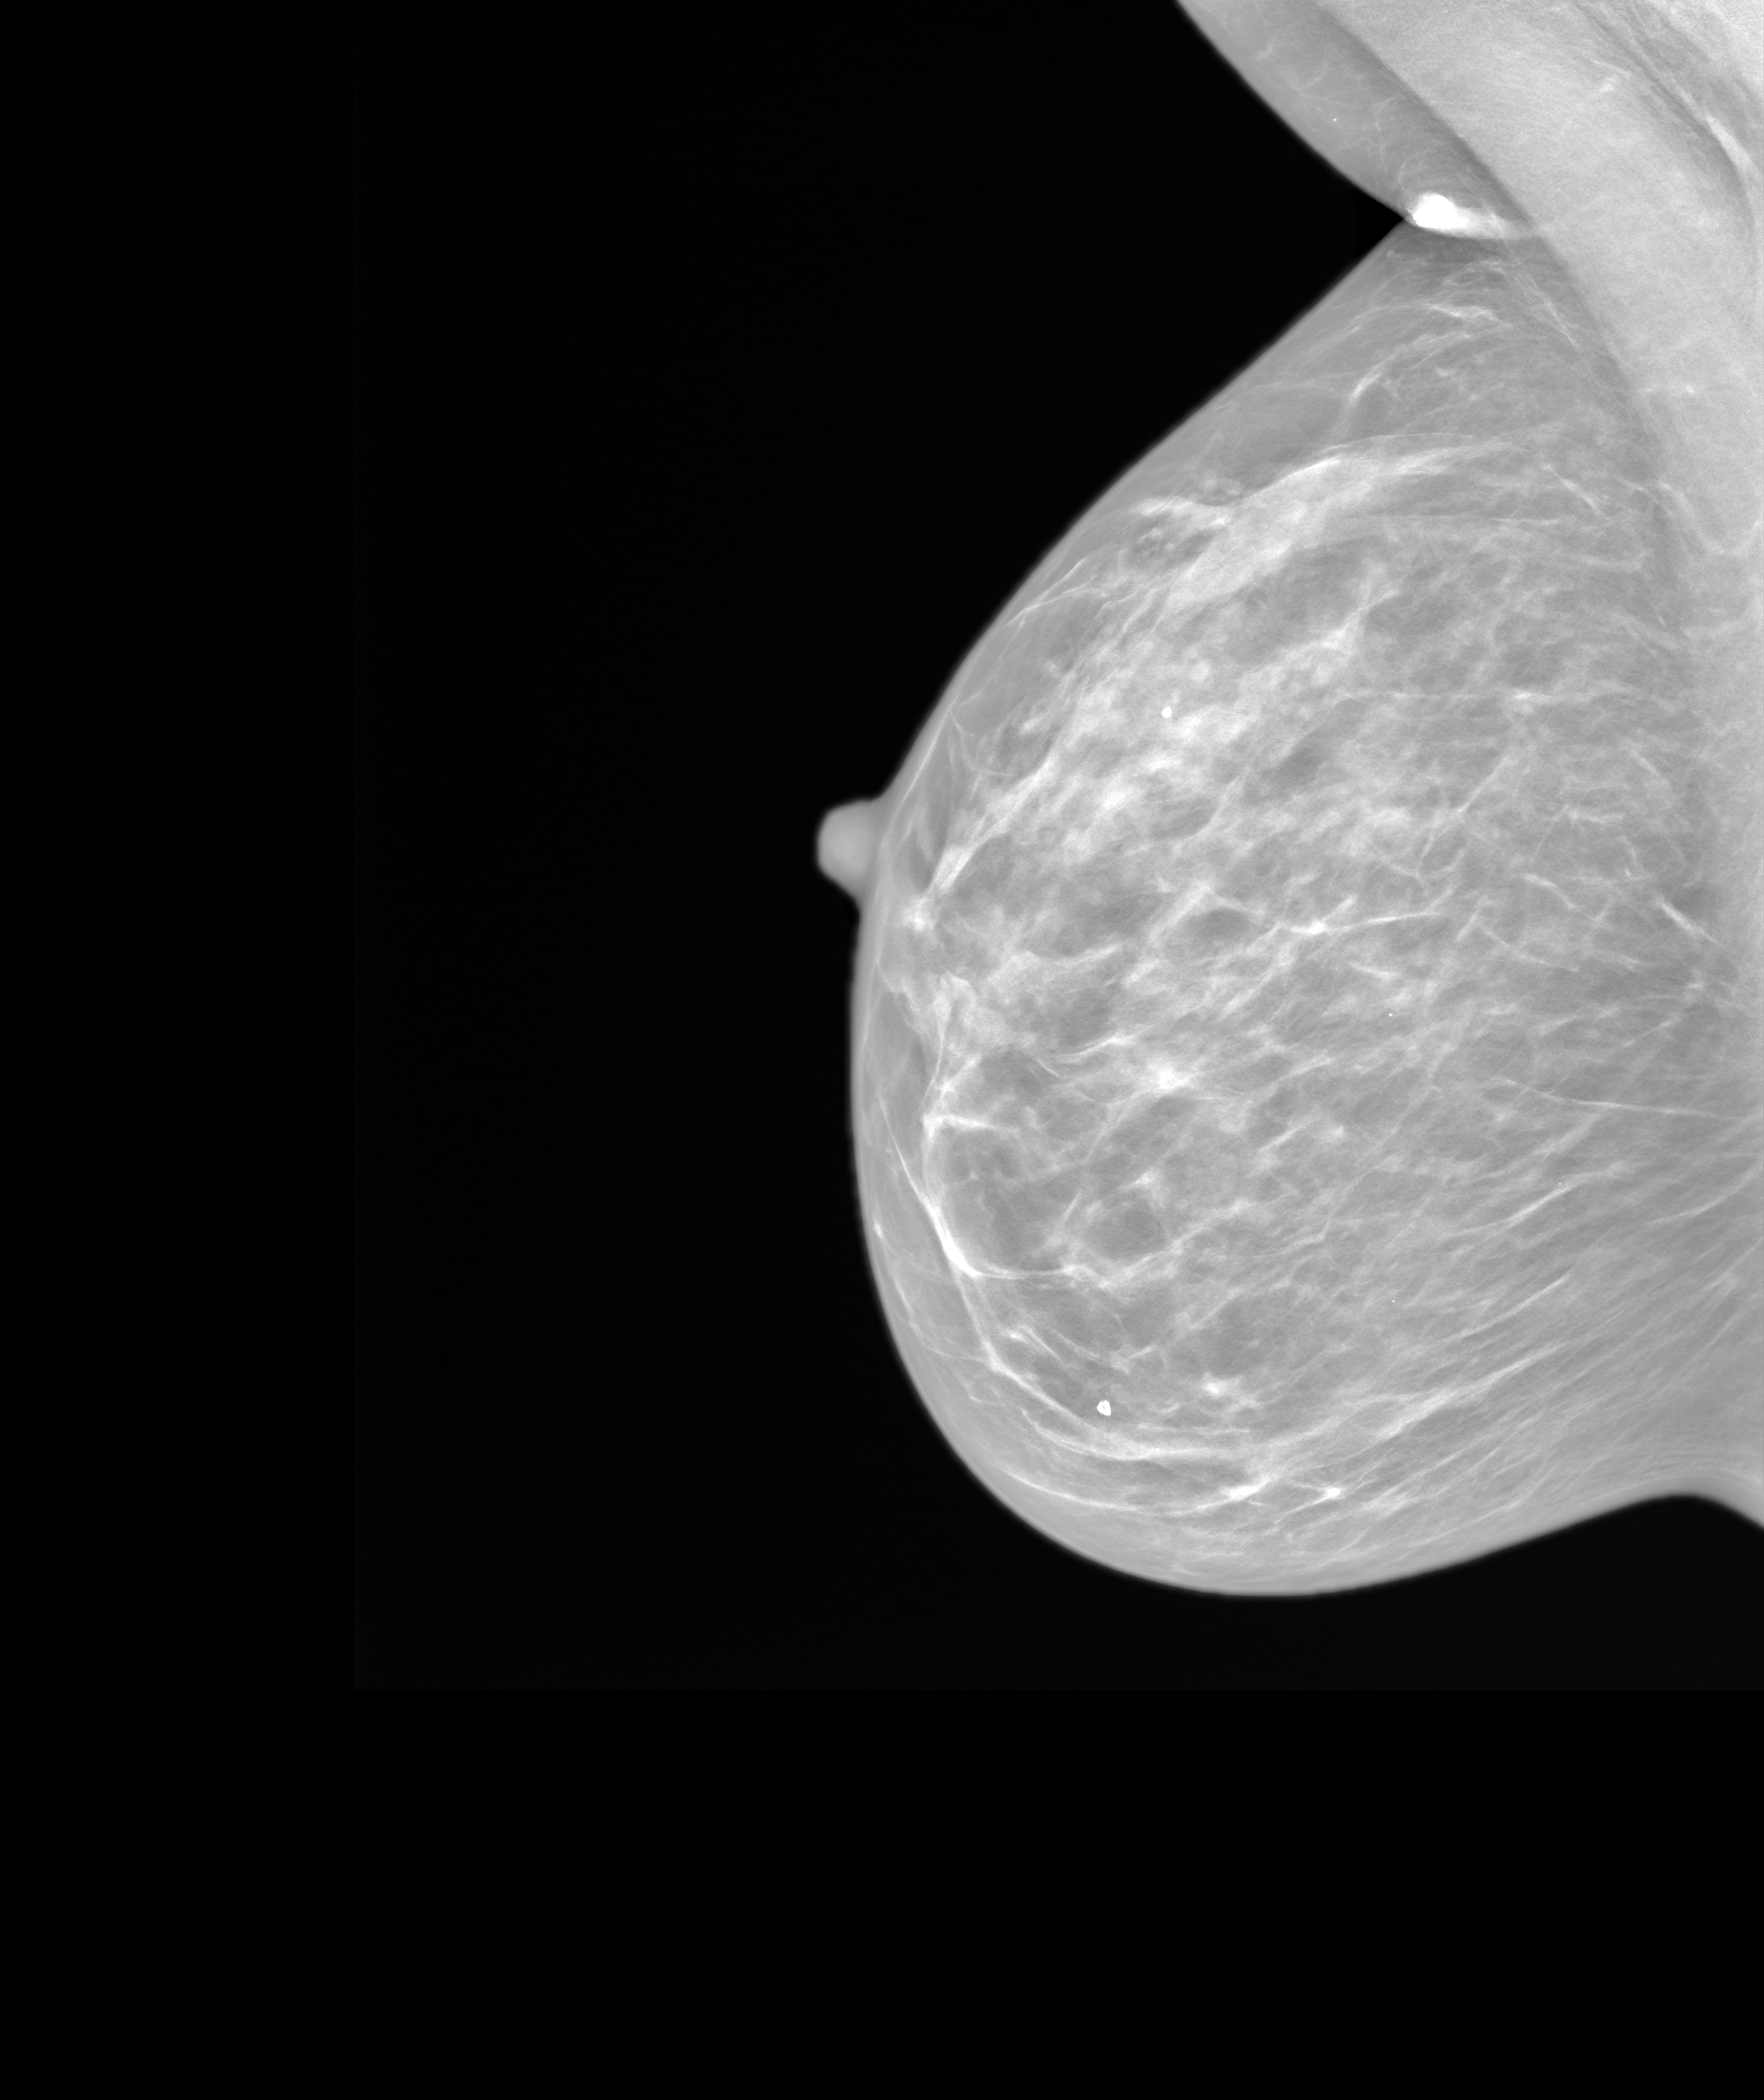
Annual screening mammography examination, system: SenoIris_1SP1.1(421). Female patient, age 57 years.
Image type: synthesized 2-D view from tomosynthesis. Breast: right. Projection: MLO view.